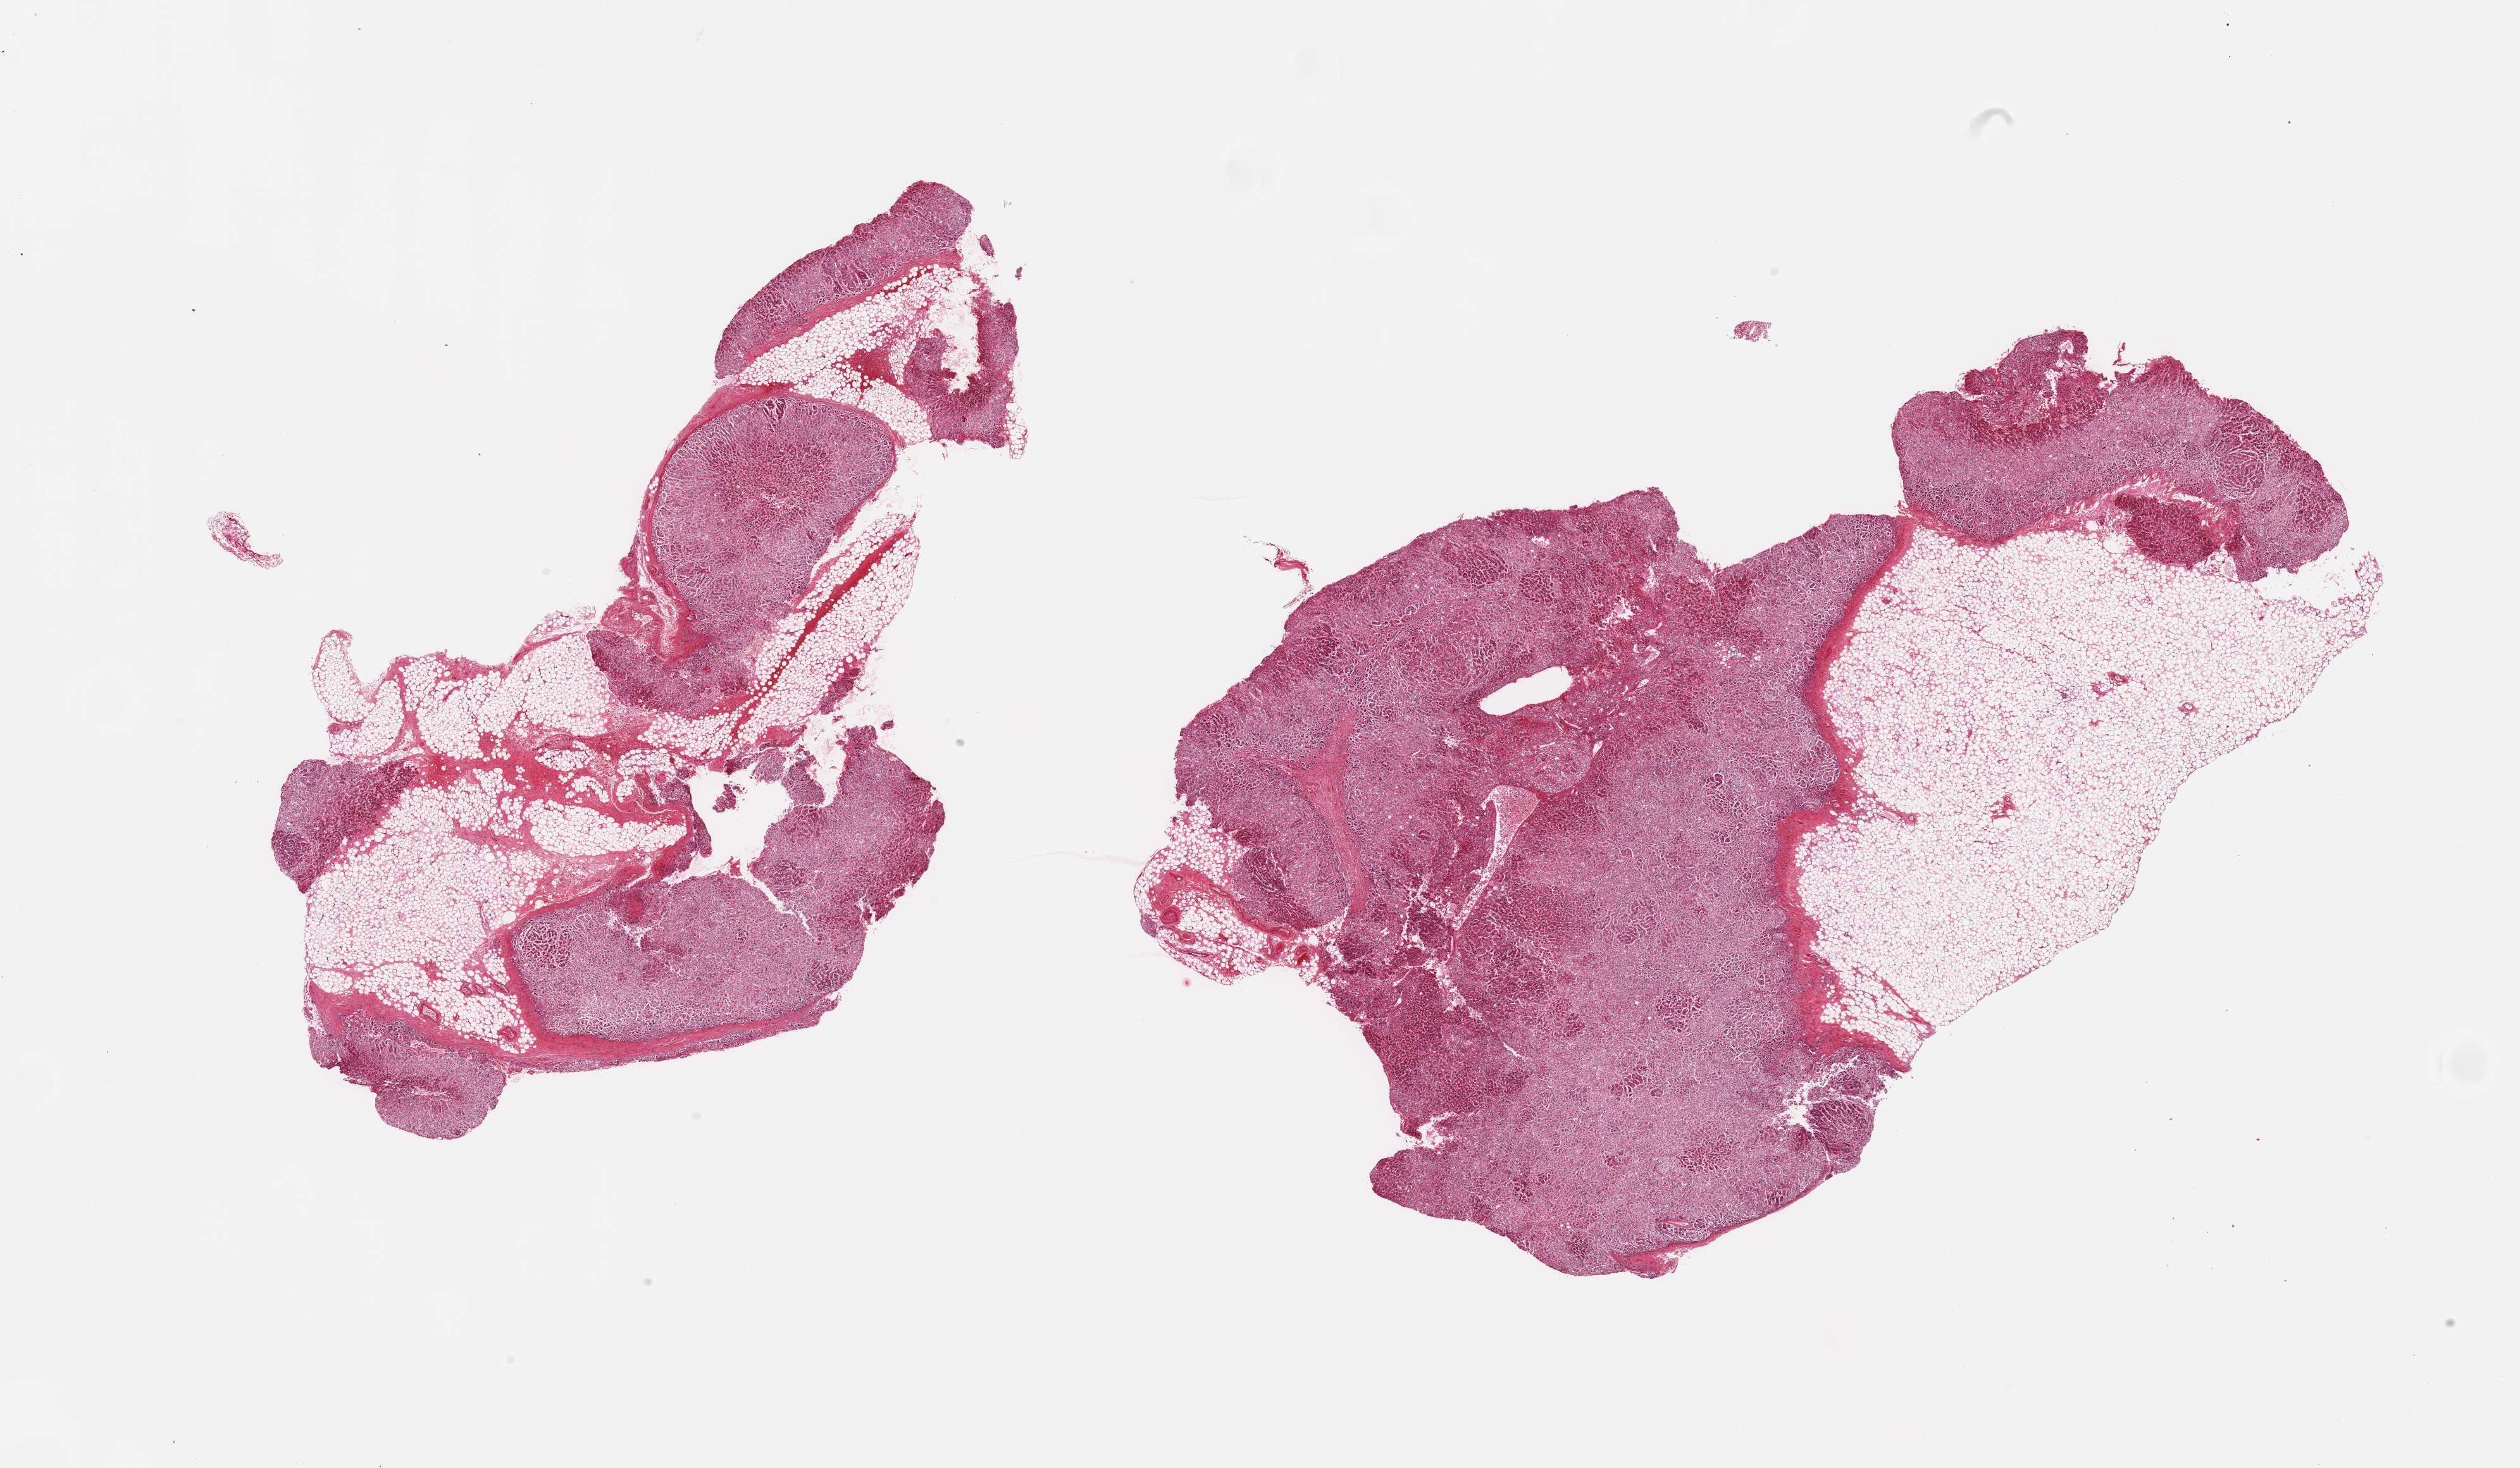
Whole-slide image, haematoxylin and eosin stain, brightfield, whole scanned area (about 31.5 x 18.4 mm) shown as a low-resolution overview; PAXgene-fixed paraffin-embedded (PFPE) section; target tissue: adrenal gland; tissue donor sample. Donor sex: male.
Reviewer comment on this tissue sample: 2 pieces, cortex, ~40-50% adherent fat.